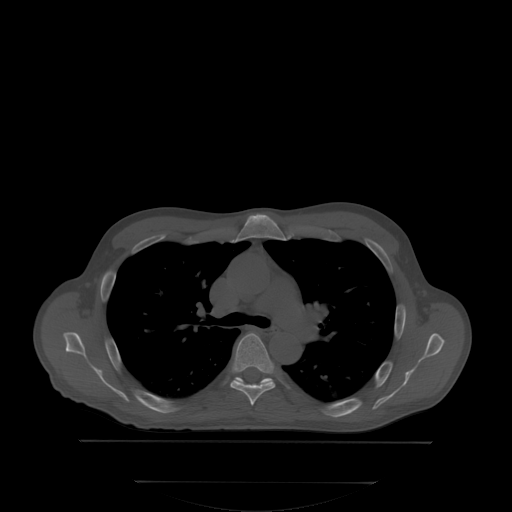
CT including the spine, one axial slice; position 246 of 350 along the scan axis; bone window (W 1800 / L 400 HU); 512 × 512 image matrix, field of view 500 × 500 mm. Male patient, age 58 years. From the clinical record (not read from this slice): primary cancer: prostate; vertebrae with lytic lesions (as recorded): L1.
Structures marked on this image (semi-automatically segmented with operator editing):
- T5 vertebra: bounding box <230,333,275,405> (left, top, right, bottom; pixels)
- T6 vertebra: <235,379,270,382>